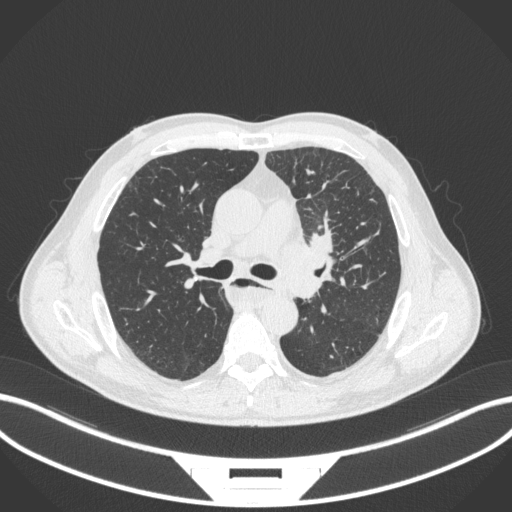
Chest CT, one axial slice; slice 234 of 411 in the series (ordered by position); reconstruction kernel B31f; 120 kVp; lung window (W 1500 / L -600 HU); 1 mm slice thickness; 512 × 512 image matrix, field of view 400 × 400 mm. Male patient, age 57 years. From the clinical record (not read from this slice): clinical TNM (as recorded): T2a N1 M0.
Outlined on this slice (bounding box drawn by a radiologist):
- lung tumour (recorded histology: squamous cell carcinoma): box from (x=274, y=223) to (x=350, y=279) px